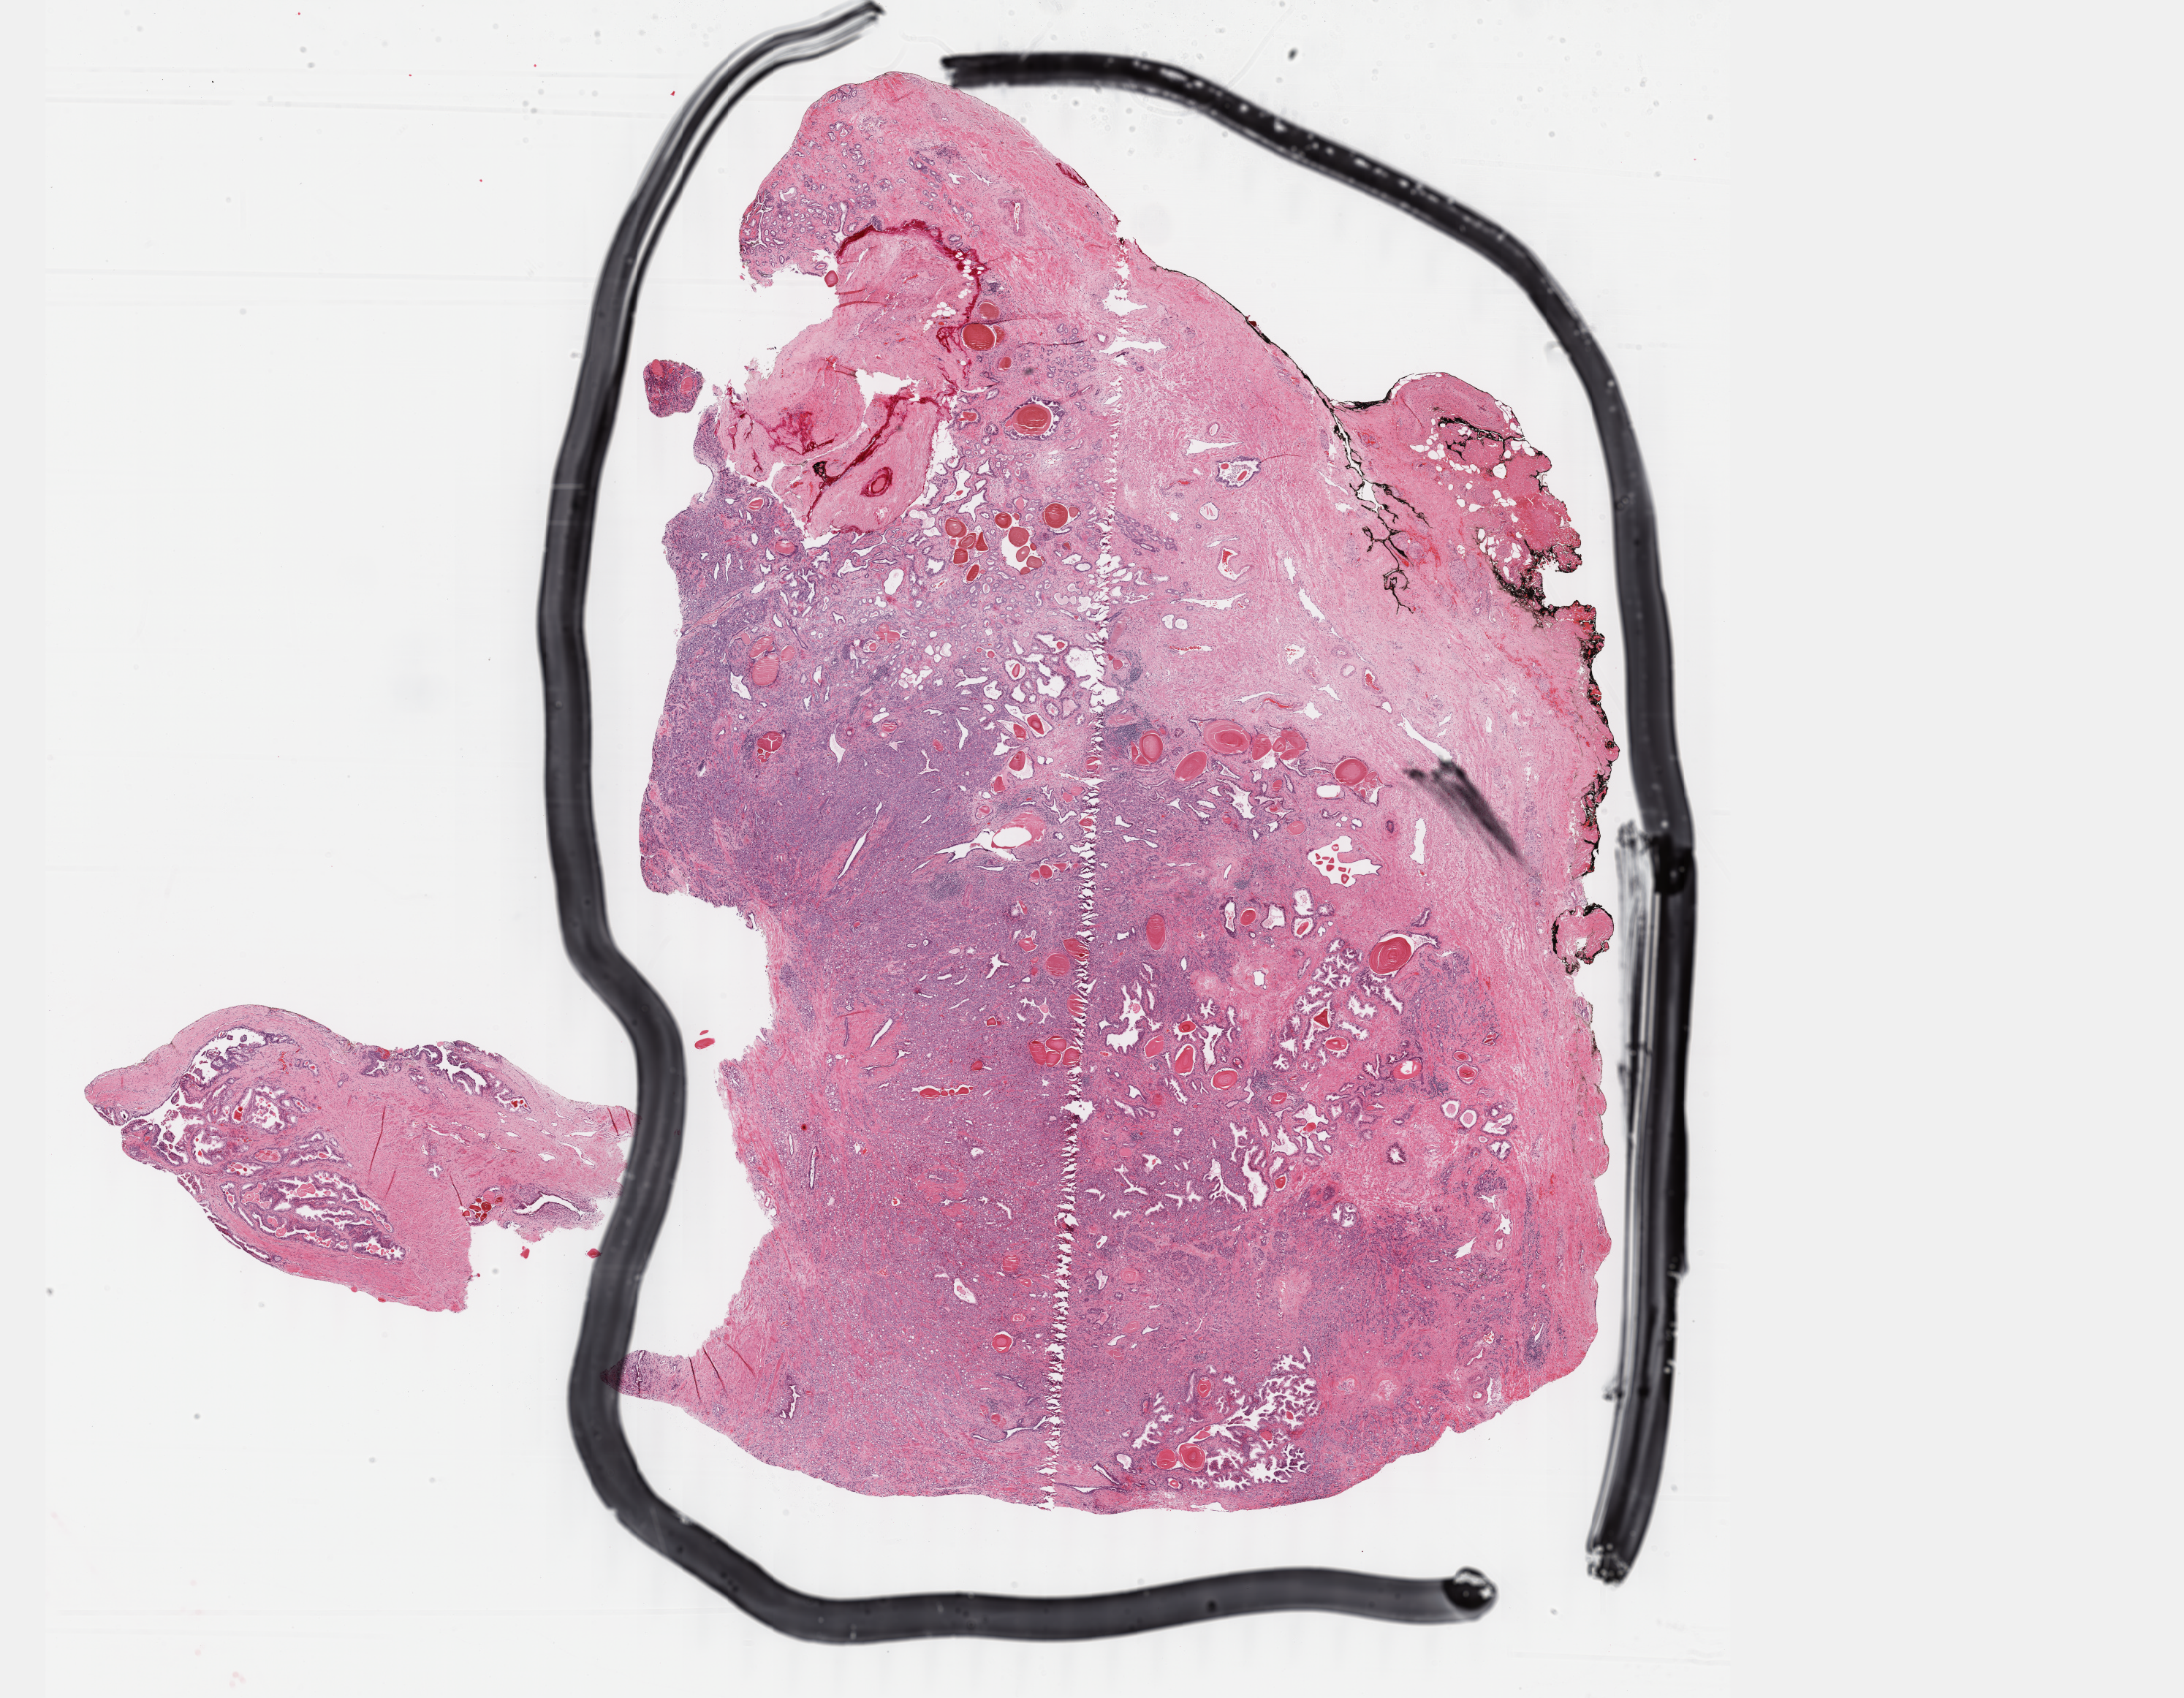
Whole-slide histology image, H&E-stained, shown as a low-resolution overview of the whole scanned area (about 23.8 x 18.5 mm, slide scanned at 40x). Formalin-fixed paraffin-embedded (FFPE) diagnostic section. Prostate, primary tumour sample. Male patient; age at initial diagnosis 68 years. Gleason score: 9 (4+5).
Pathologic diagnosis: Adenocarcinoma, NOS (prostate gland).